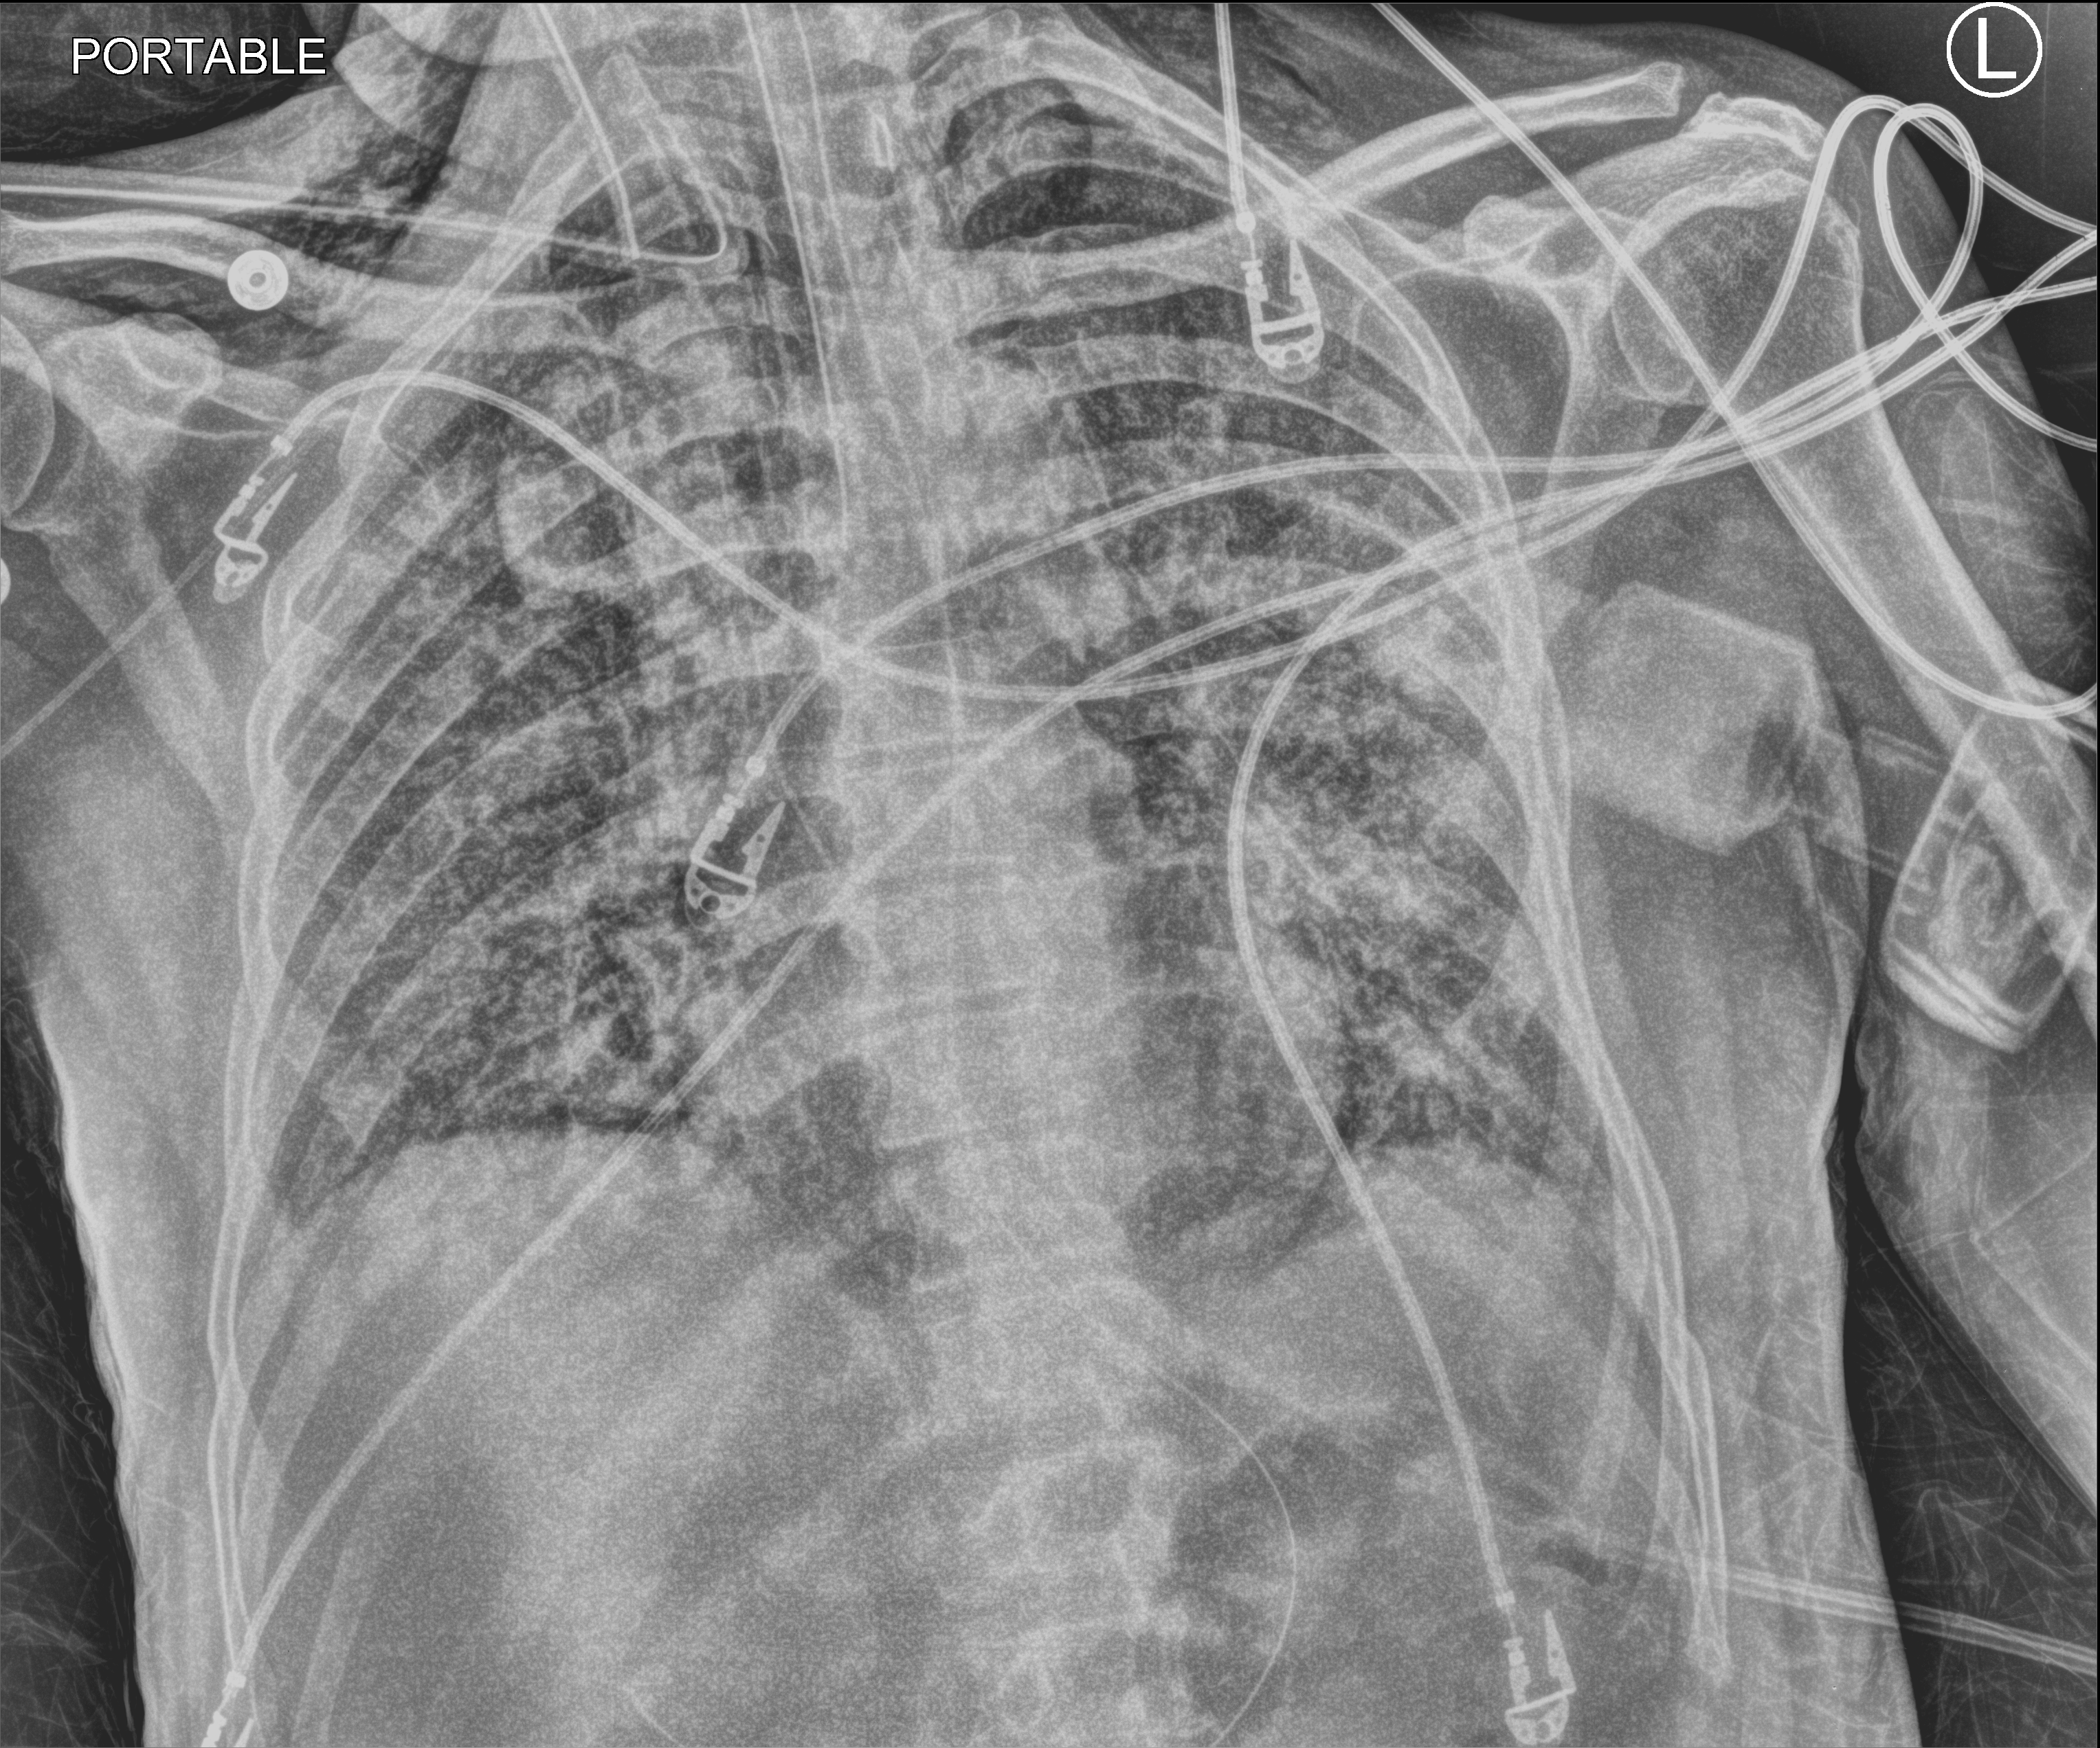
Chest X-ray (portable), anteroposterior (AP) projection. Patient hospitalised with COVID-19; male, aged 60–74 years.
Admission-level facts for this patient (not findings on this image; timing relative to this image not recorded): mechanically ventilated during this hospital stay: yes; chronic kidney disease (admission record): no; smoking status (admission record): never.